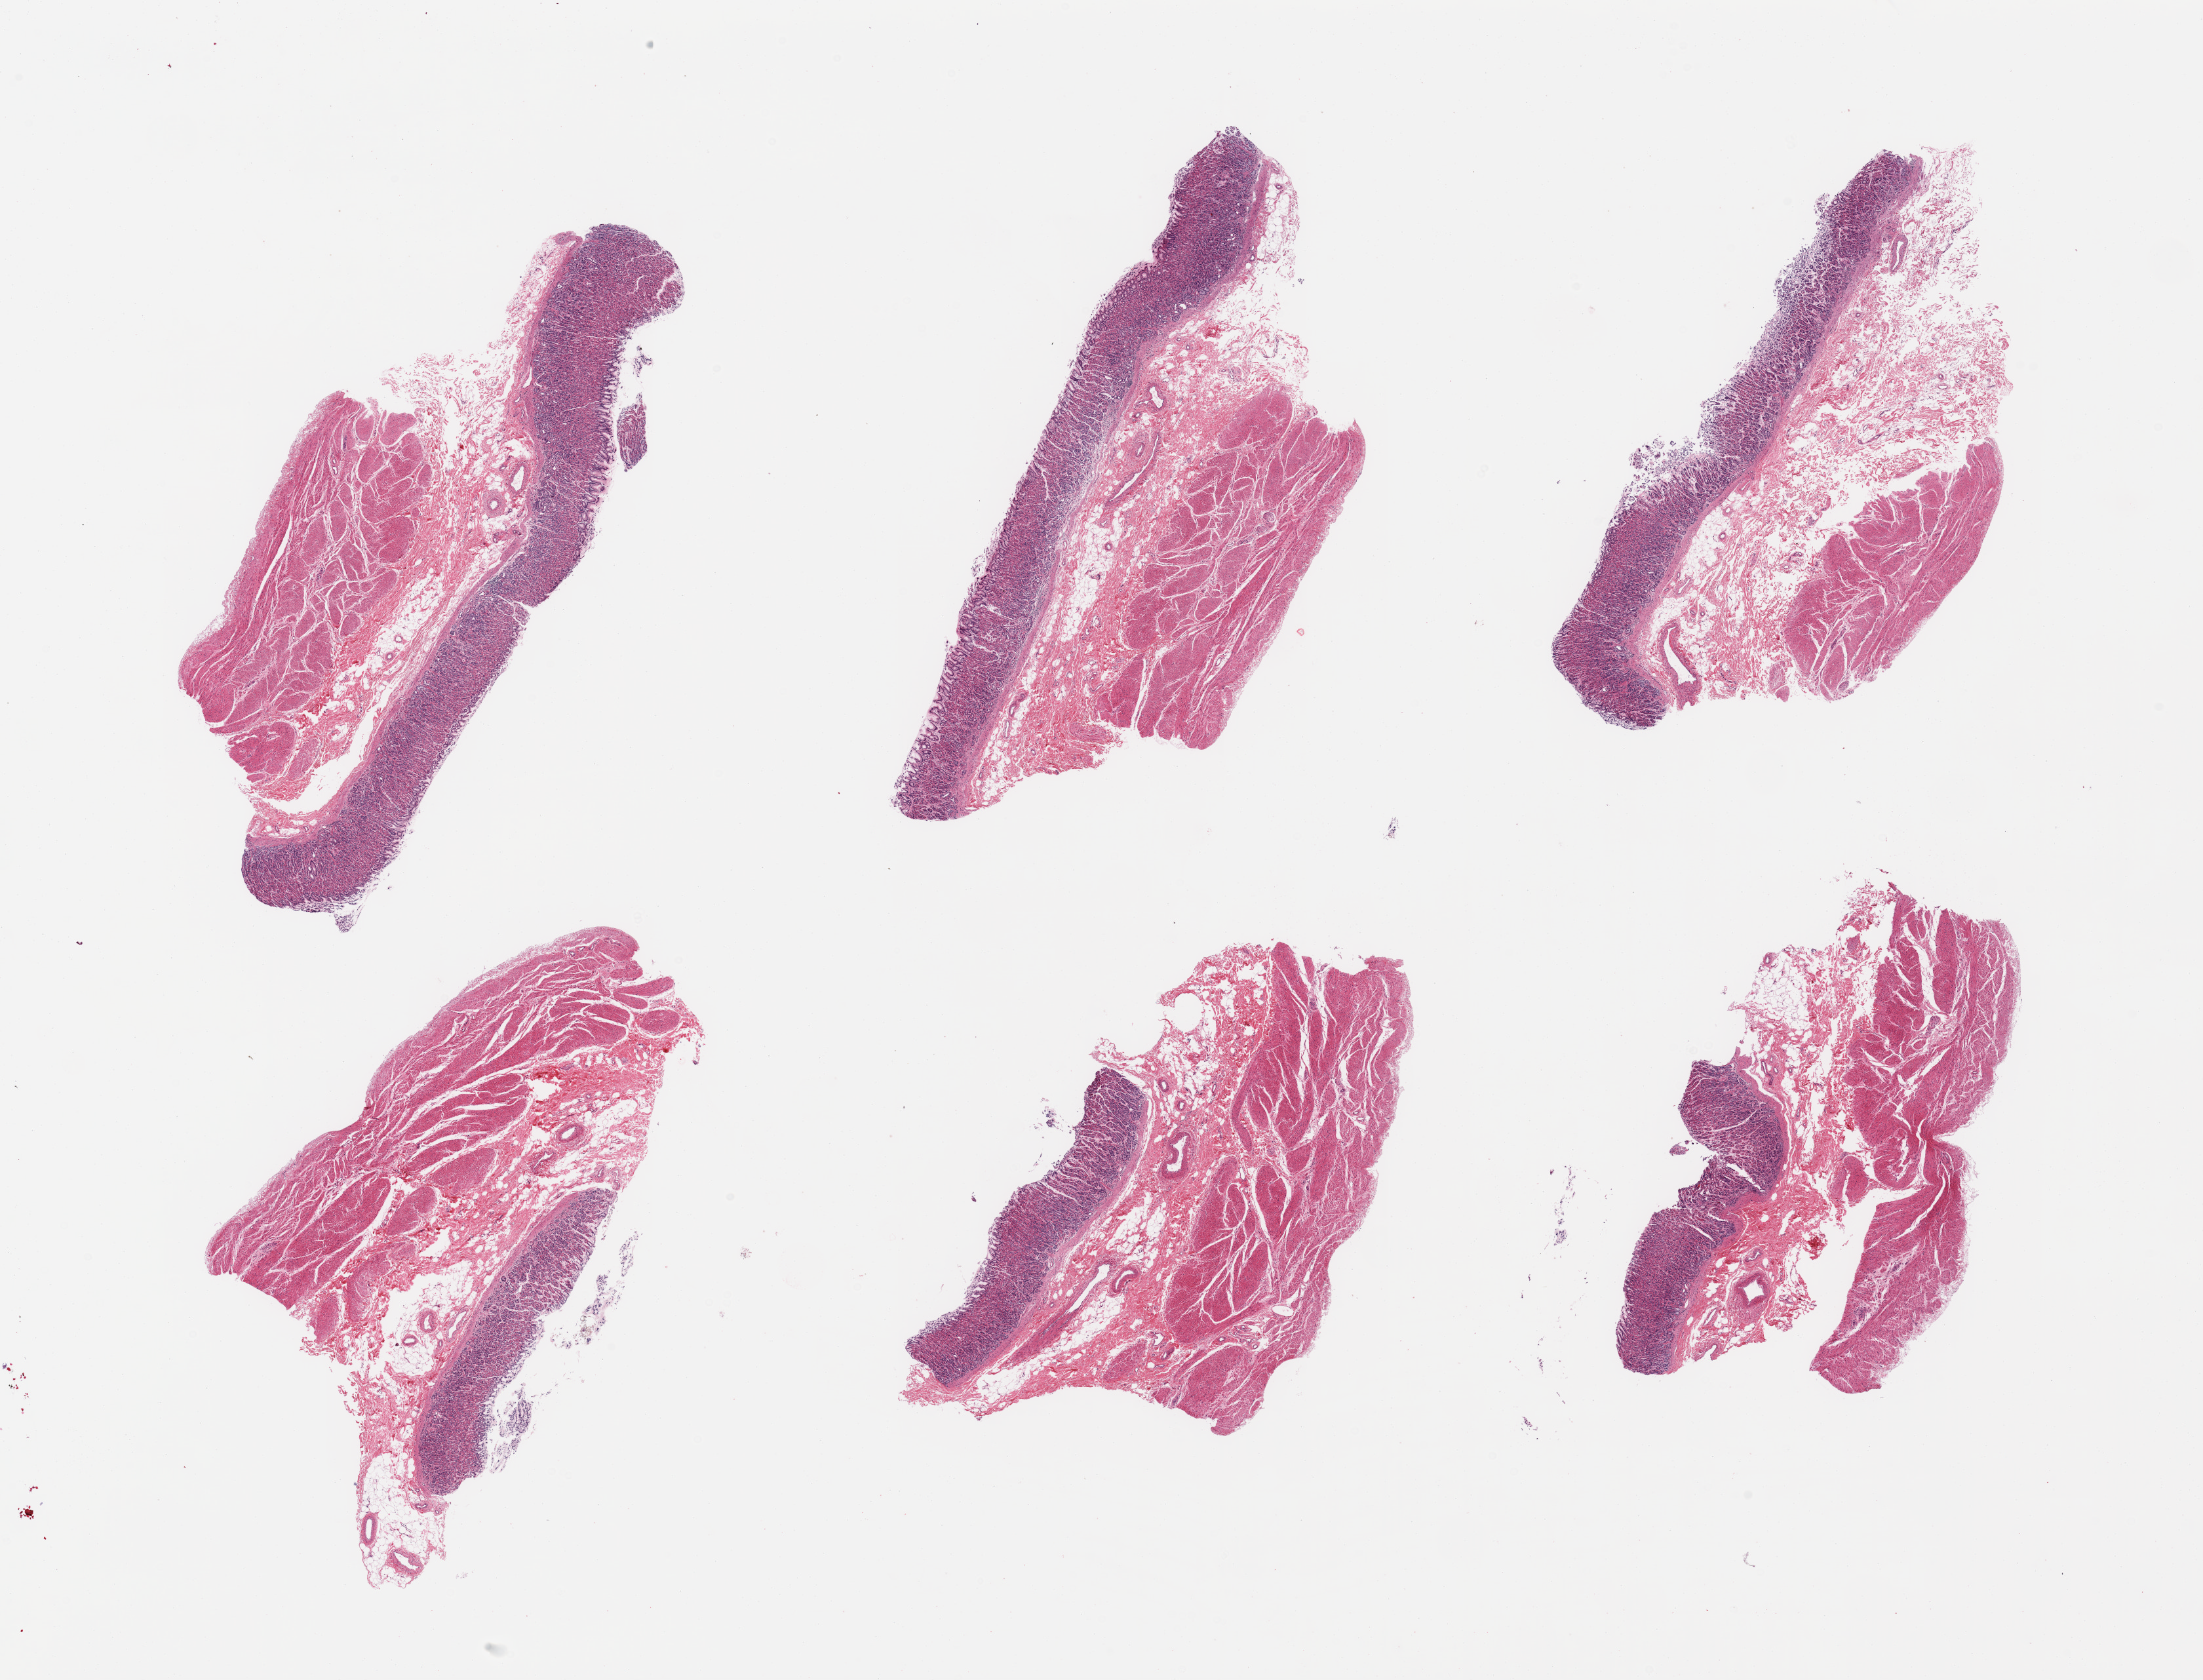
Digitized H&E-stained section, whole scanned area (about 26.6 x 20.3 mm, from a 20x scan) shown as a low-resolution overview, PAXgene-fixed, paraffin-embedded tissue, sampled site (target tissue): stomach, donor tissue sample. Male donor.
Pathologist's review note for this sample: 6 pieces; full thickness sections.